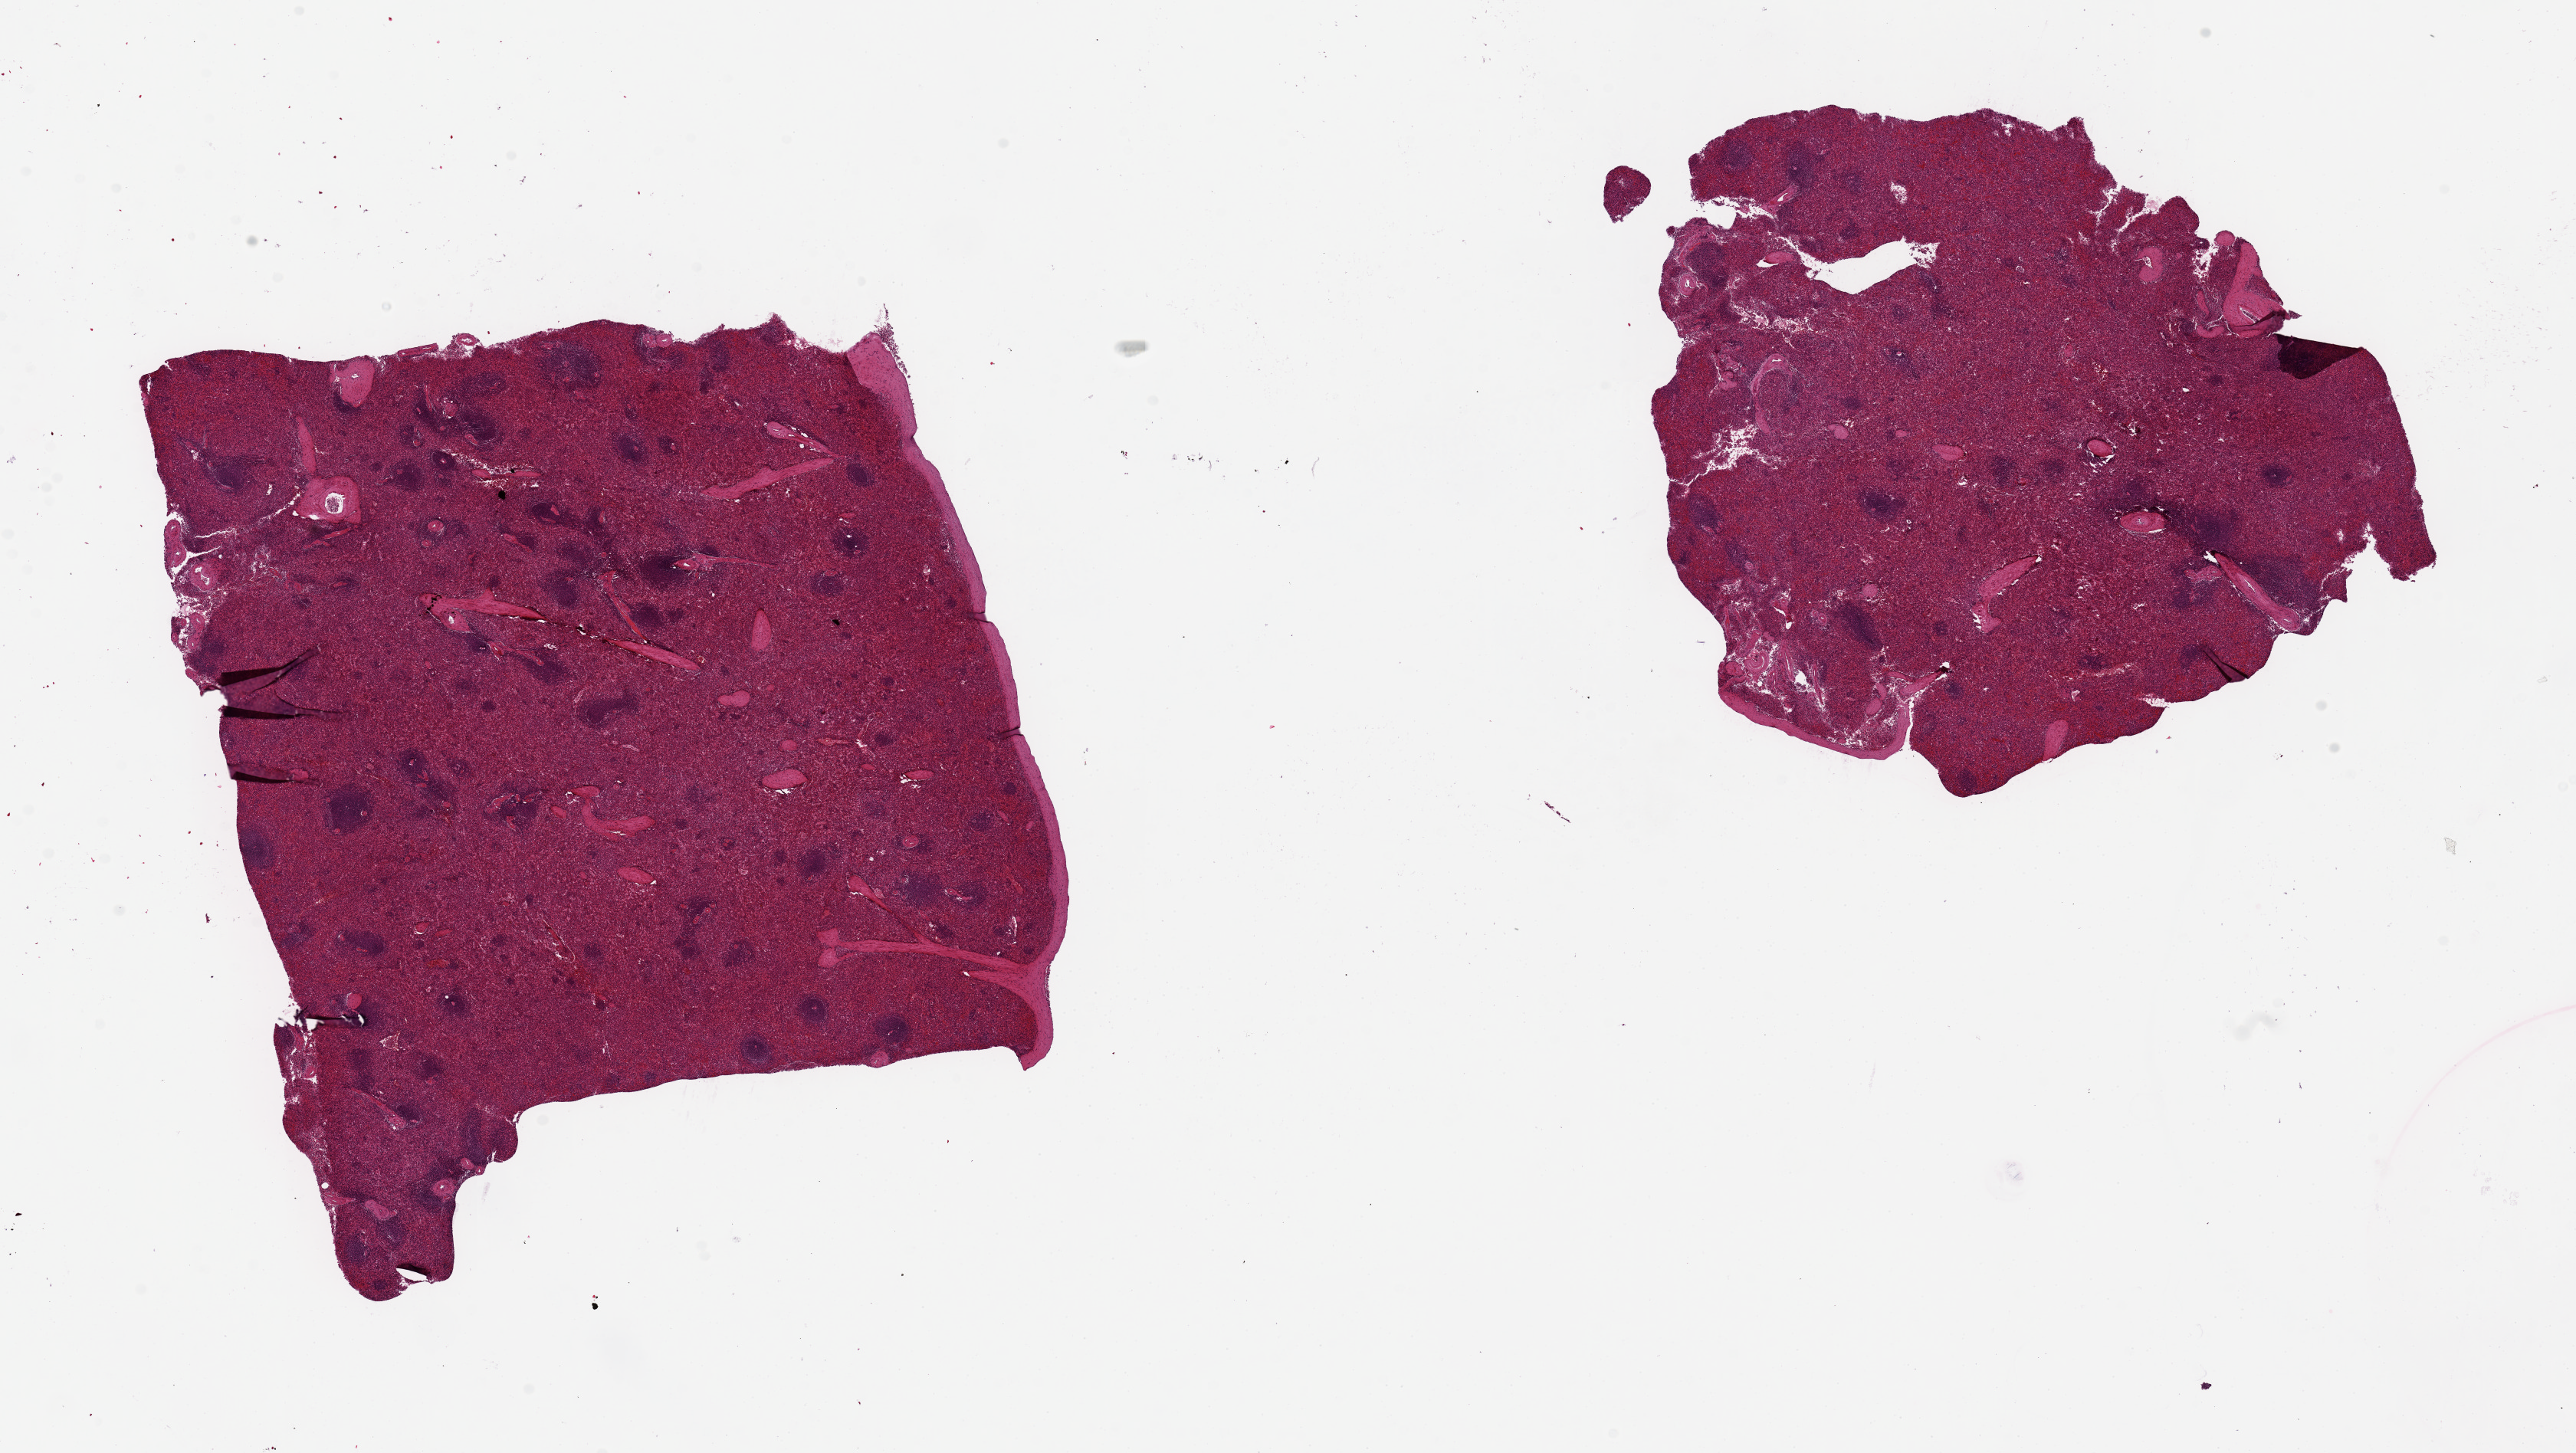
Whole-slide image, hematoxylin and eosin (H&E) stain, brightfield, low-resolution overview of the scanned area, about 26.6 x 15.0 mm, PAXgene-fixed, paraffin-embedded tissue, sampled site (target tissue): spleen, donor tissue sample. Donor sex: male.
Pathologist's review note for this sample: 2 pieces ~8x8mm.